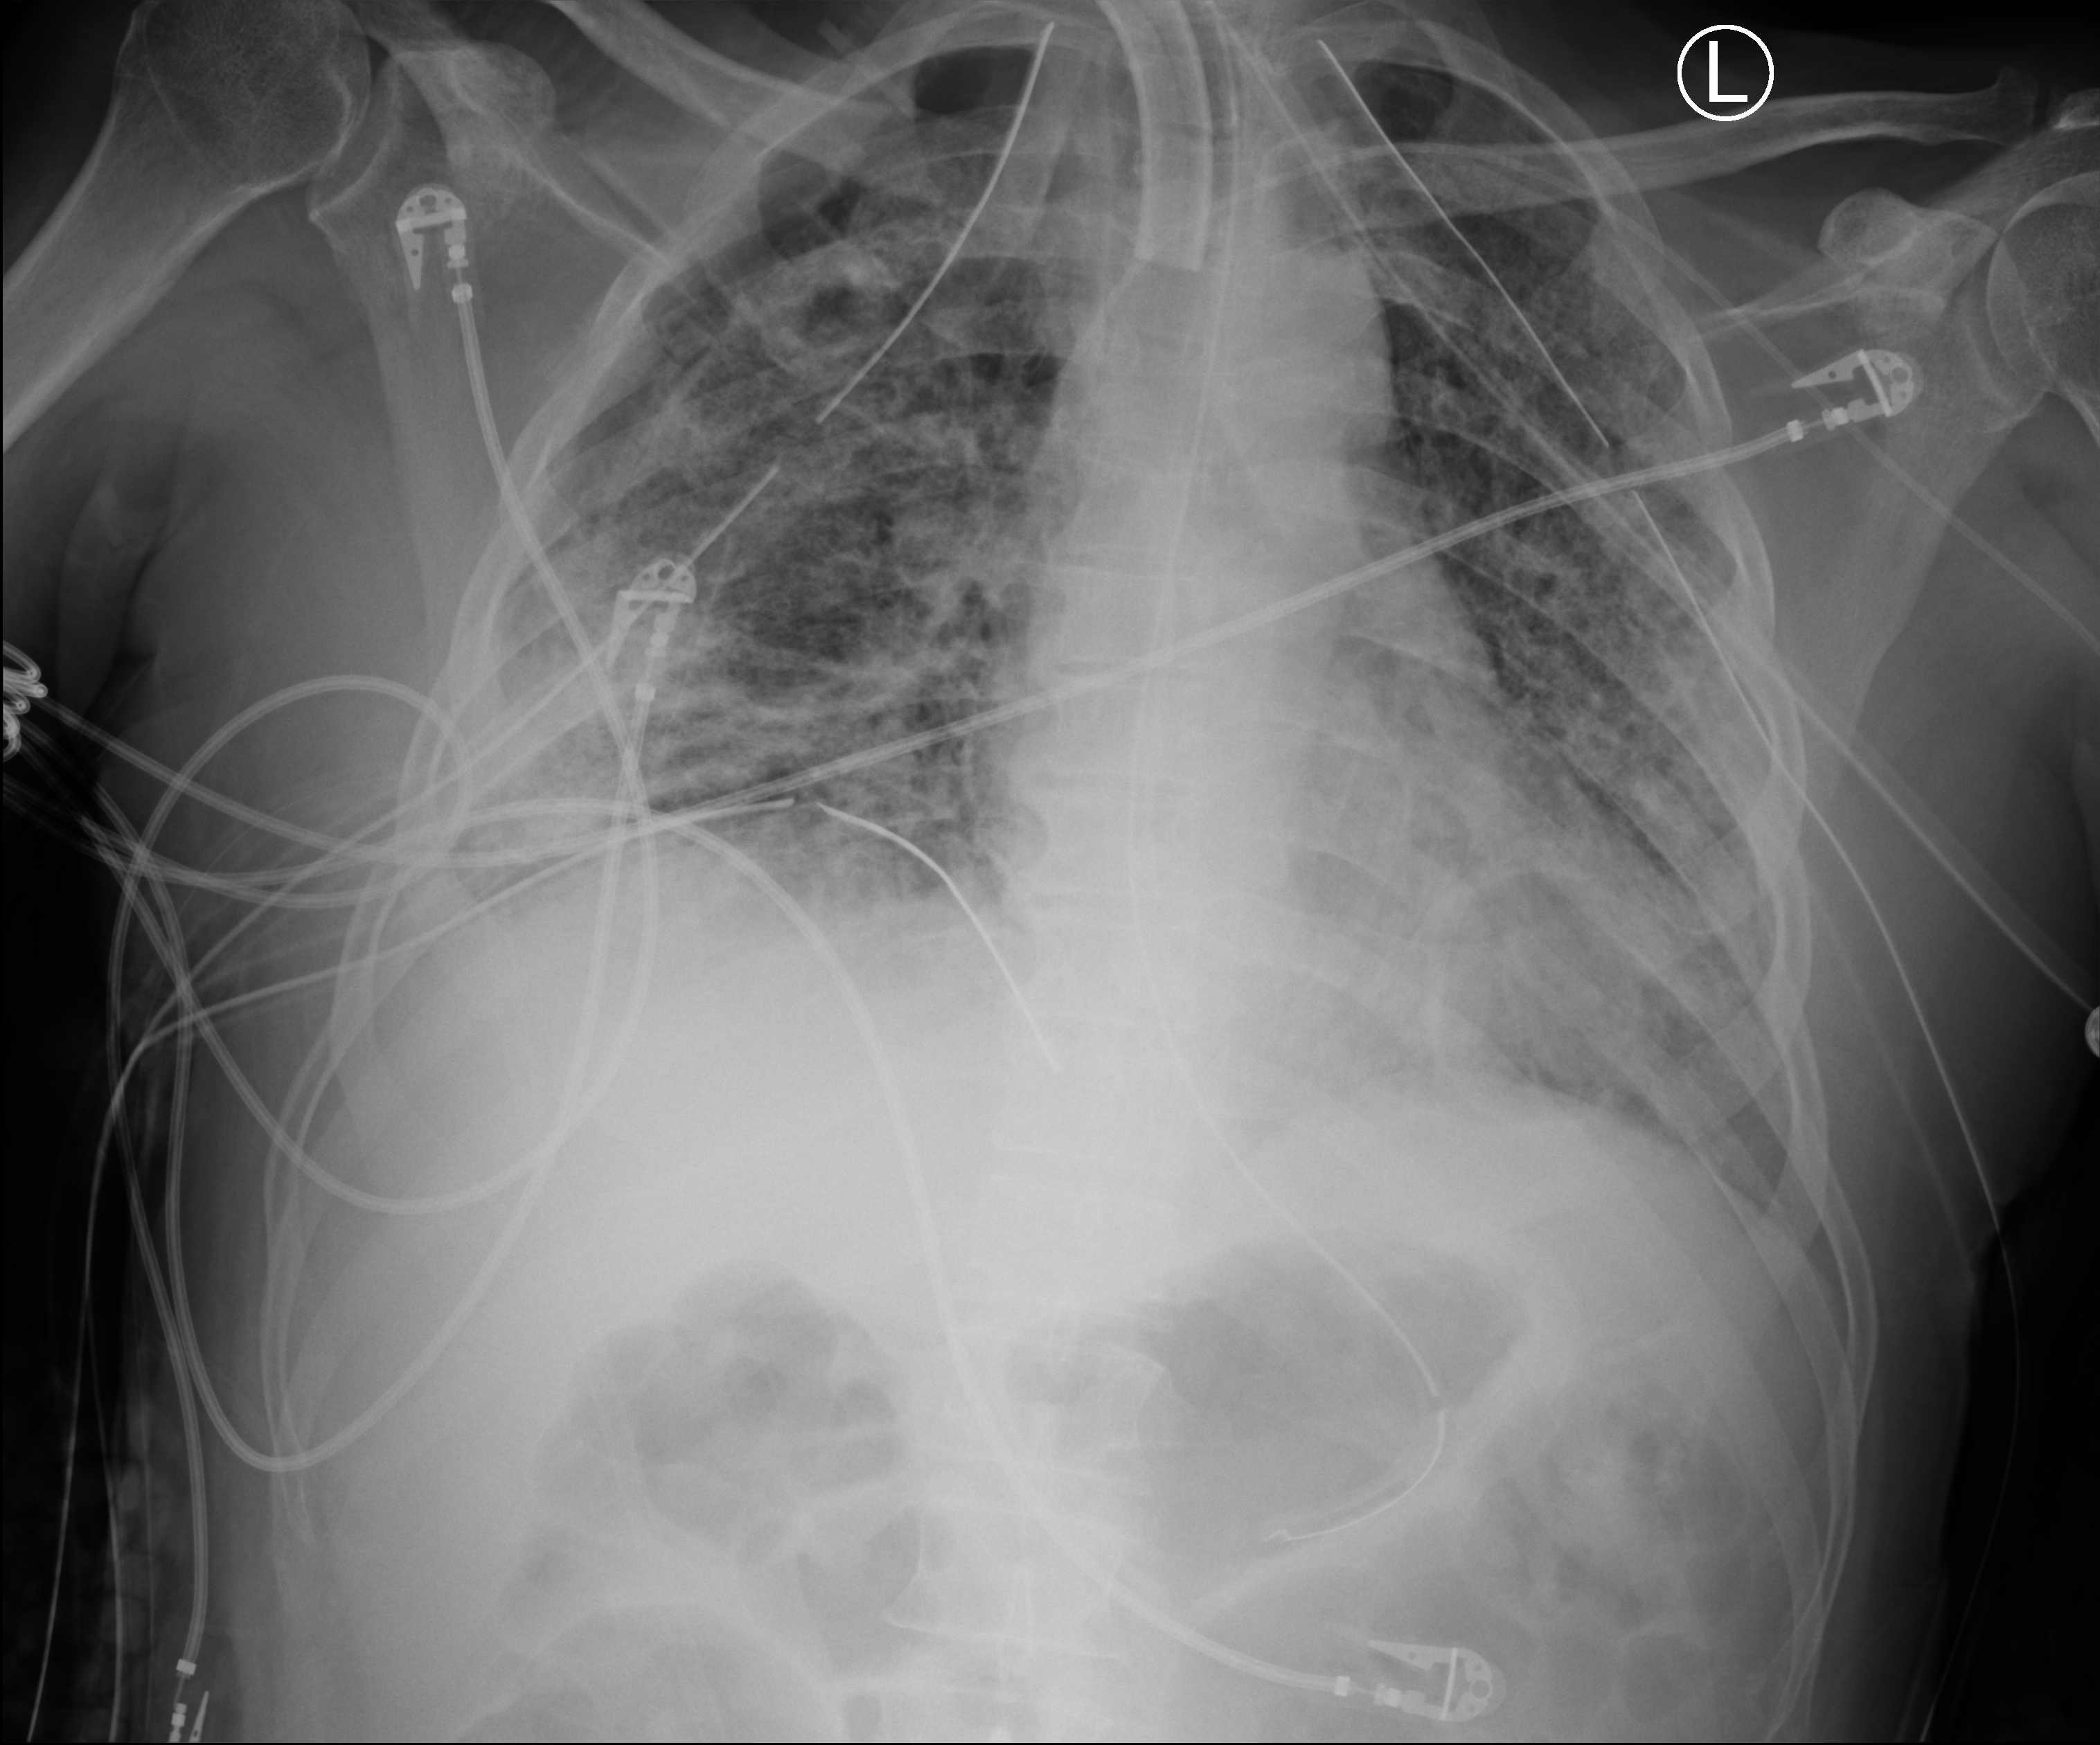
Portable chest radiograph; anteroposterior (AP) projection. Male patient hospitalised with COVID-19, age 18–59 years.
Admission-level facts for this patient (not findings on this image; timing relative to this image not recorded): length of hospital stay: 83 days; mechanically ventilated during this hospital stay: yes; COPD (admission record): no.